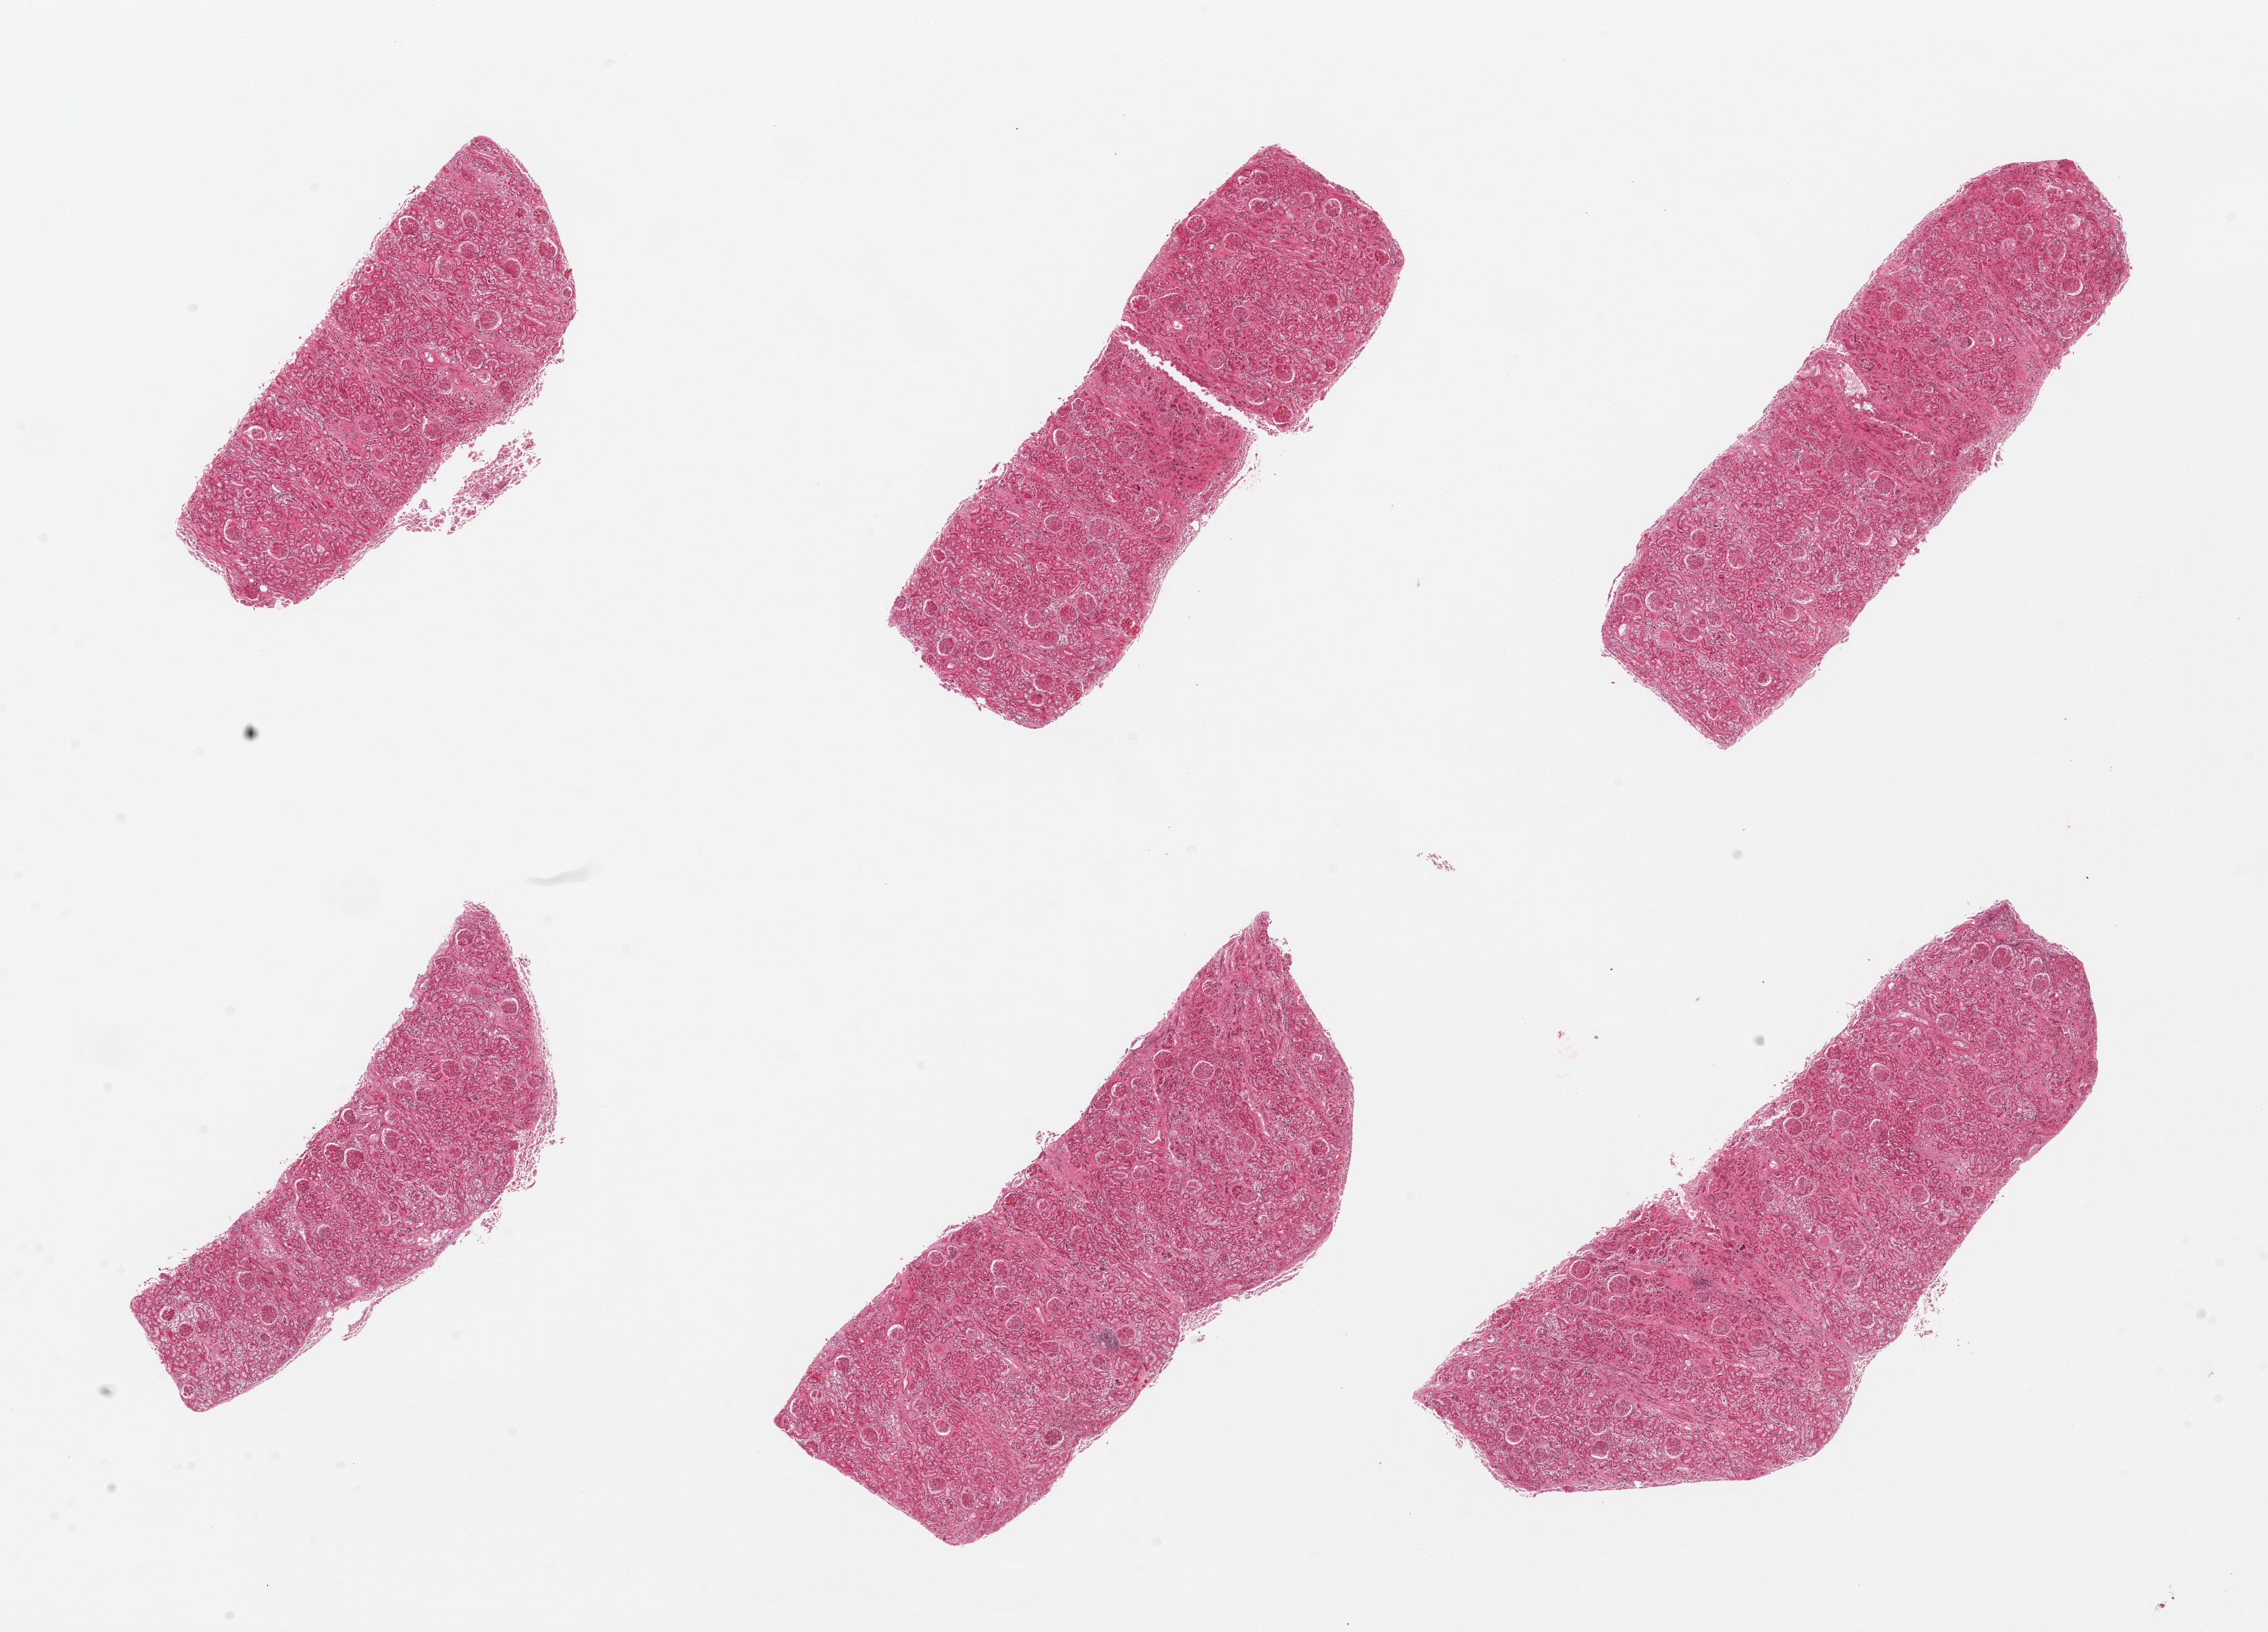
Haematoxylin and eosin whole-slide image, whole scanned area (about 26.6 x 19.1 mm, acquisition: 20x scan) shown as a low-resolution overview. PAXgene-fixed, paraffin-embedded tissue. Target tissue: renal cortex. Tissue donor sample. Male donor.
Pathologist's review note for this sample: 6 pieces; no active or chronic lesions.